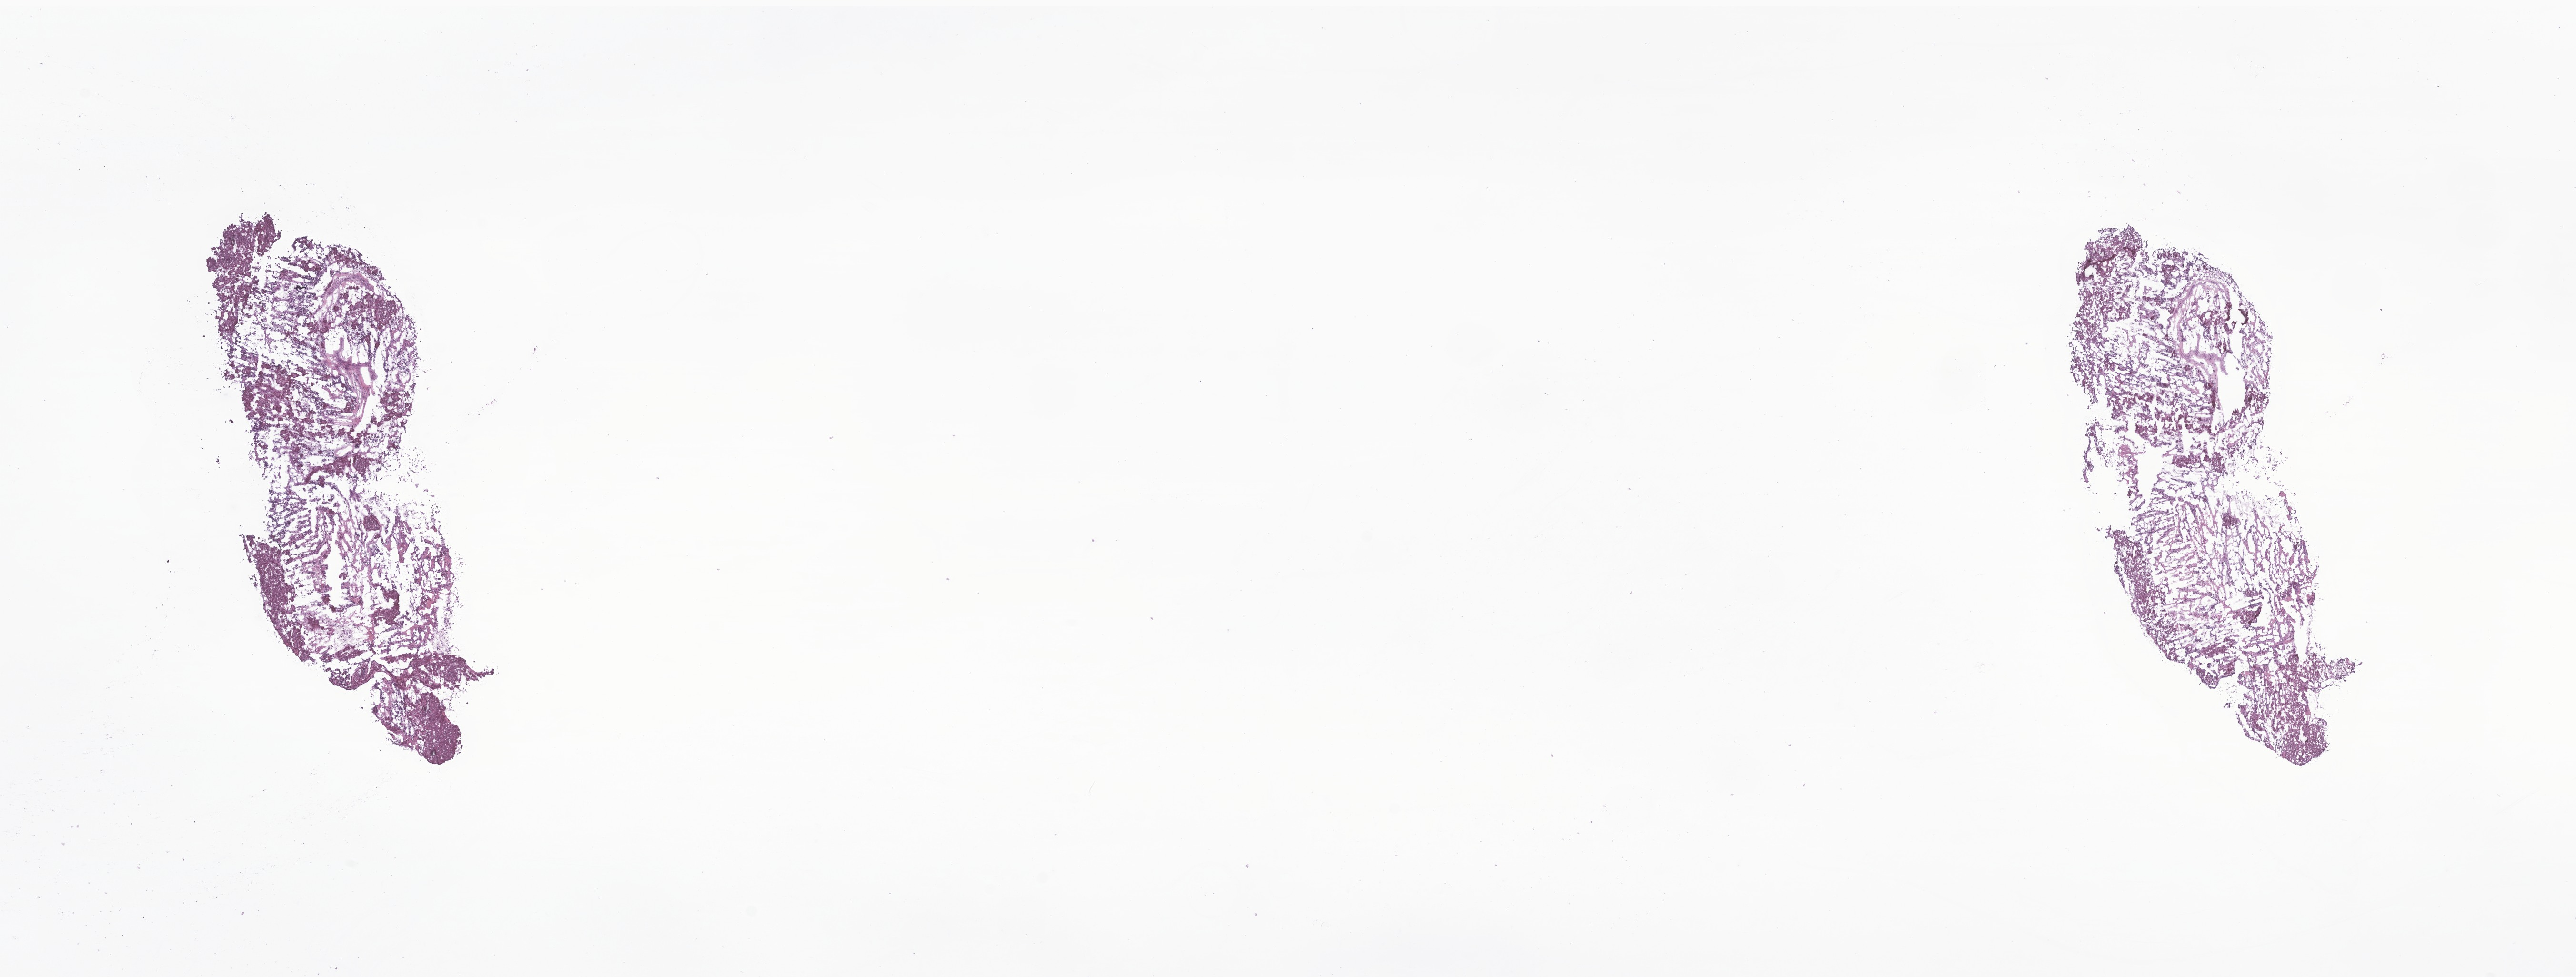
Whole-slide image, haematoxylin and eosin stain of tumor tissue from the retroperitoneum, whole scanned area (about 22.8 x 8.6 mm) shown as a low-resolution overview, frozen section. Female patient, age 478 days (about 1.3 years).
Diagnosis: Neuroblastoma, NOS.